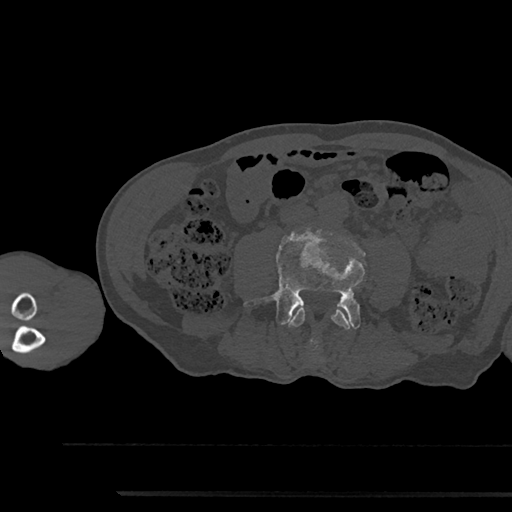
CT including the spine, one axial slice; slice 437 of 797 in the series (ordered by position); reconstruction kernel Br40s/3; bone window (W 1800 / L 400 HU); 0.5 mm slice thickness; 512 × 512 image matrix. Male patient, age 79 years. Case-level facts recorded for this patient, not image findings: primary cancer: prostate.
Annotated regions visible in this slice (semi-automatically segmented with operator editing):
- L3 vertebra: bounding box (x1, y1, x2, y2) in pixels: (288, 306, 351, 330)
- L4 vertebra: (244, 227, 365, 349)